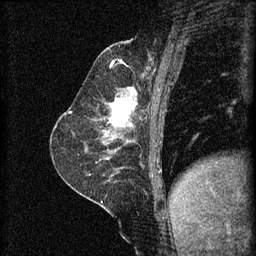
Breast MRI (dynamic contrast-enhanced), one sagittal slice. Slice 25 of 60 in the series (ordered by position). 3 images stored at this slice position (order not interpretable as contrast timing). 1.5 T. TE 4.2 ms, TR 8.2 ms. 256 × 256 image matrix. Female patient, age 59 years.
Outlined on this slice (semi-automatic segmentation, software-assisted and operator-edited):
- analysis volume of interest (the breast-tissue region the enhancement analysis was run in; not a lesion): bounding box (x1, y1, x2, y2) in pixels: (102, 92, 137, 135)
- tumour enhancement mask (voxels above the 70 % enhancement threshold inside the analysis volume of interest): (110, 92, 137, 127)